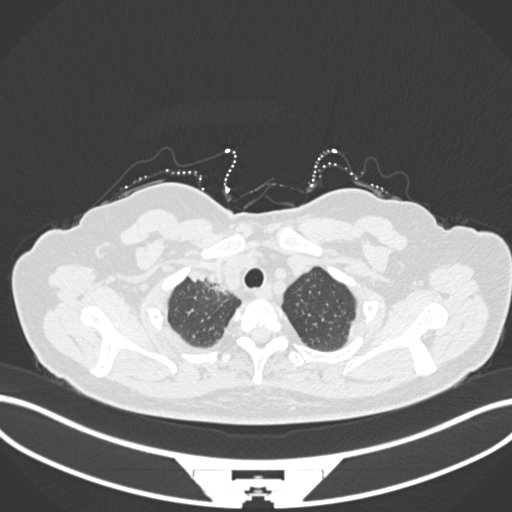
Chest CT, one axial slice. Position 151 of 172 along the scan axis. 120 kVp. Lung window (W 1500 / L -600 HU). 512 × 512 image matrix, field of view 400 × 400 mm. Patient: female, 52 years. From the clinical record (not read from this slice): clinical TNM (as recorded): T3 N1 M1.
Structures marked on this image (bounding box drawn by a radiologist):
- lung tumour (recorded histology: adenocarcinoma): bounding box <185,268,226,293> (left, top, right, bottom; pixels)